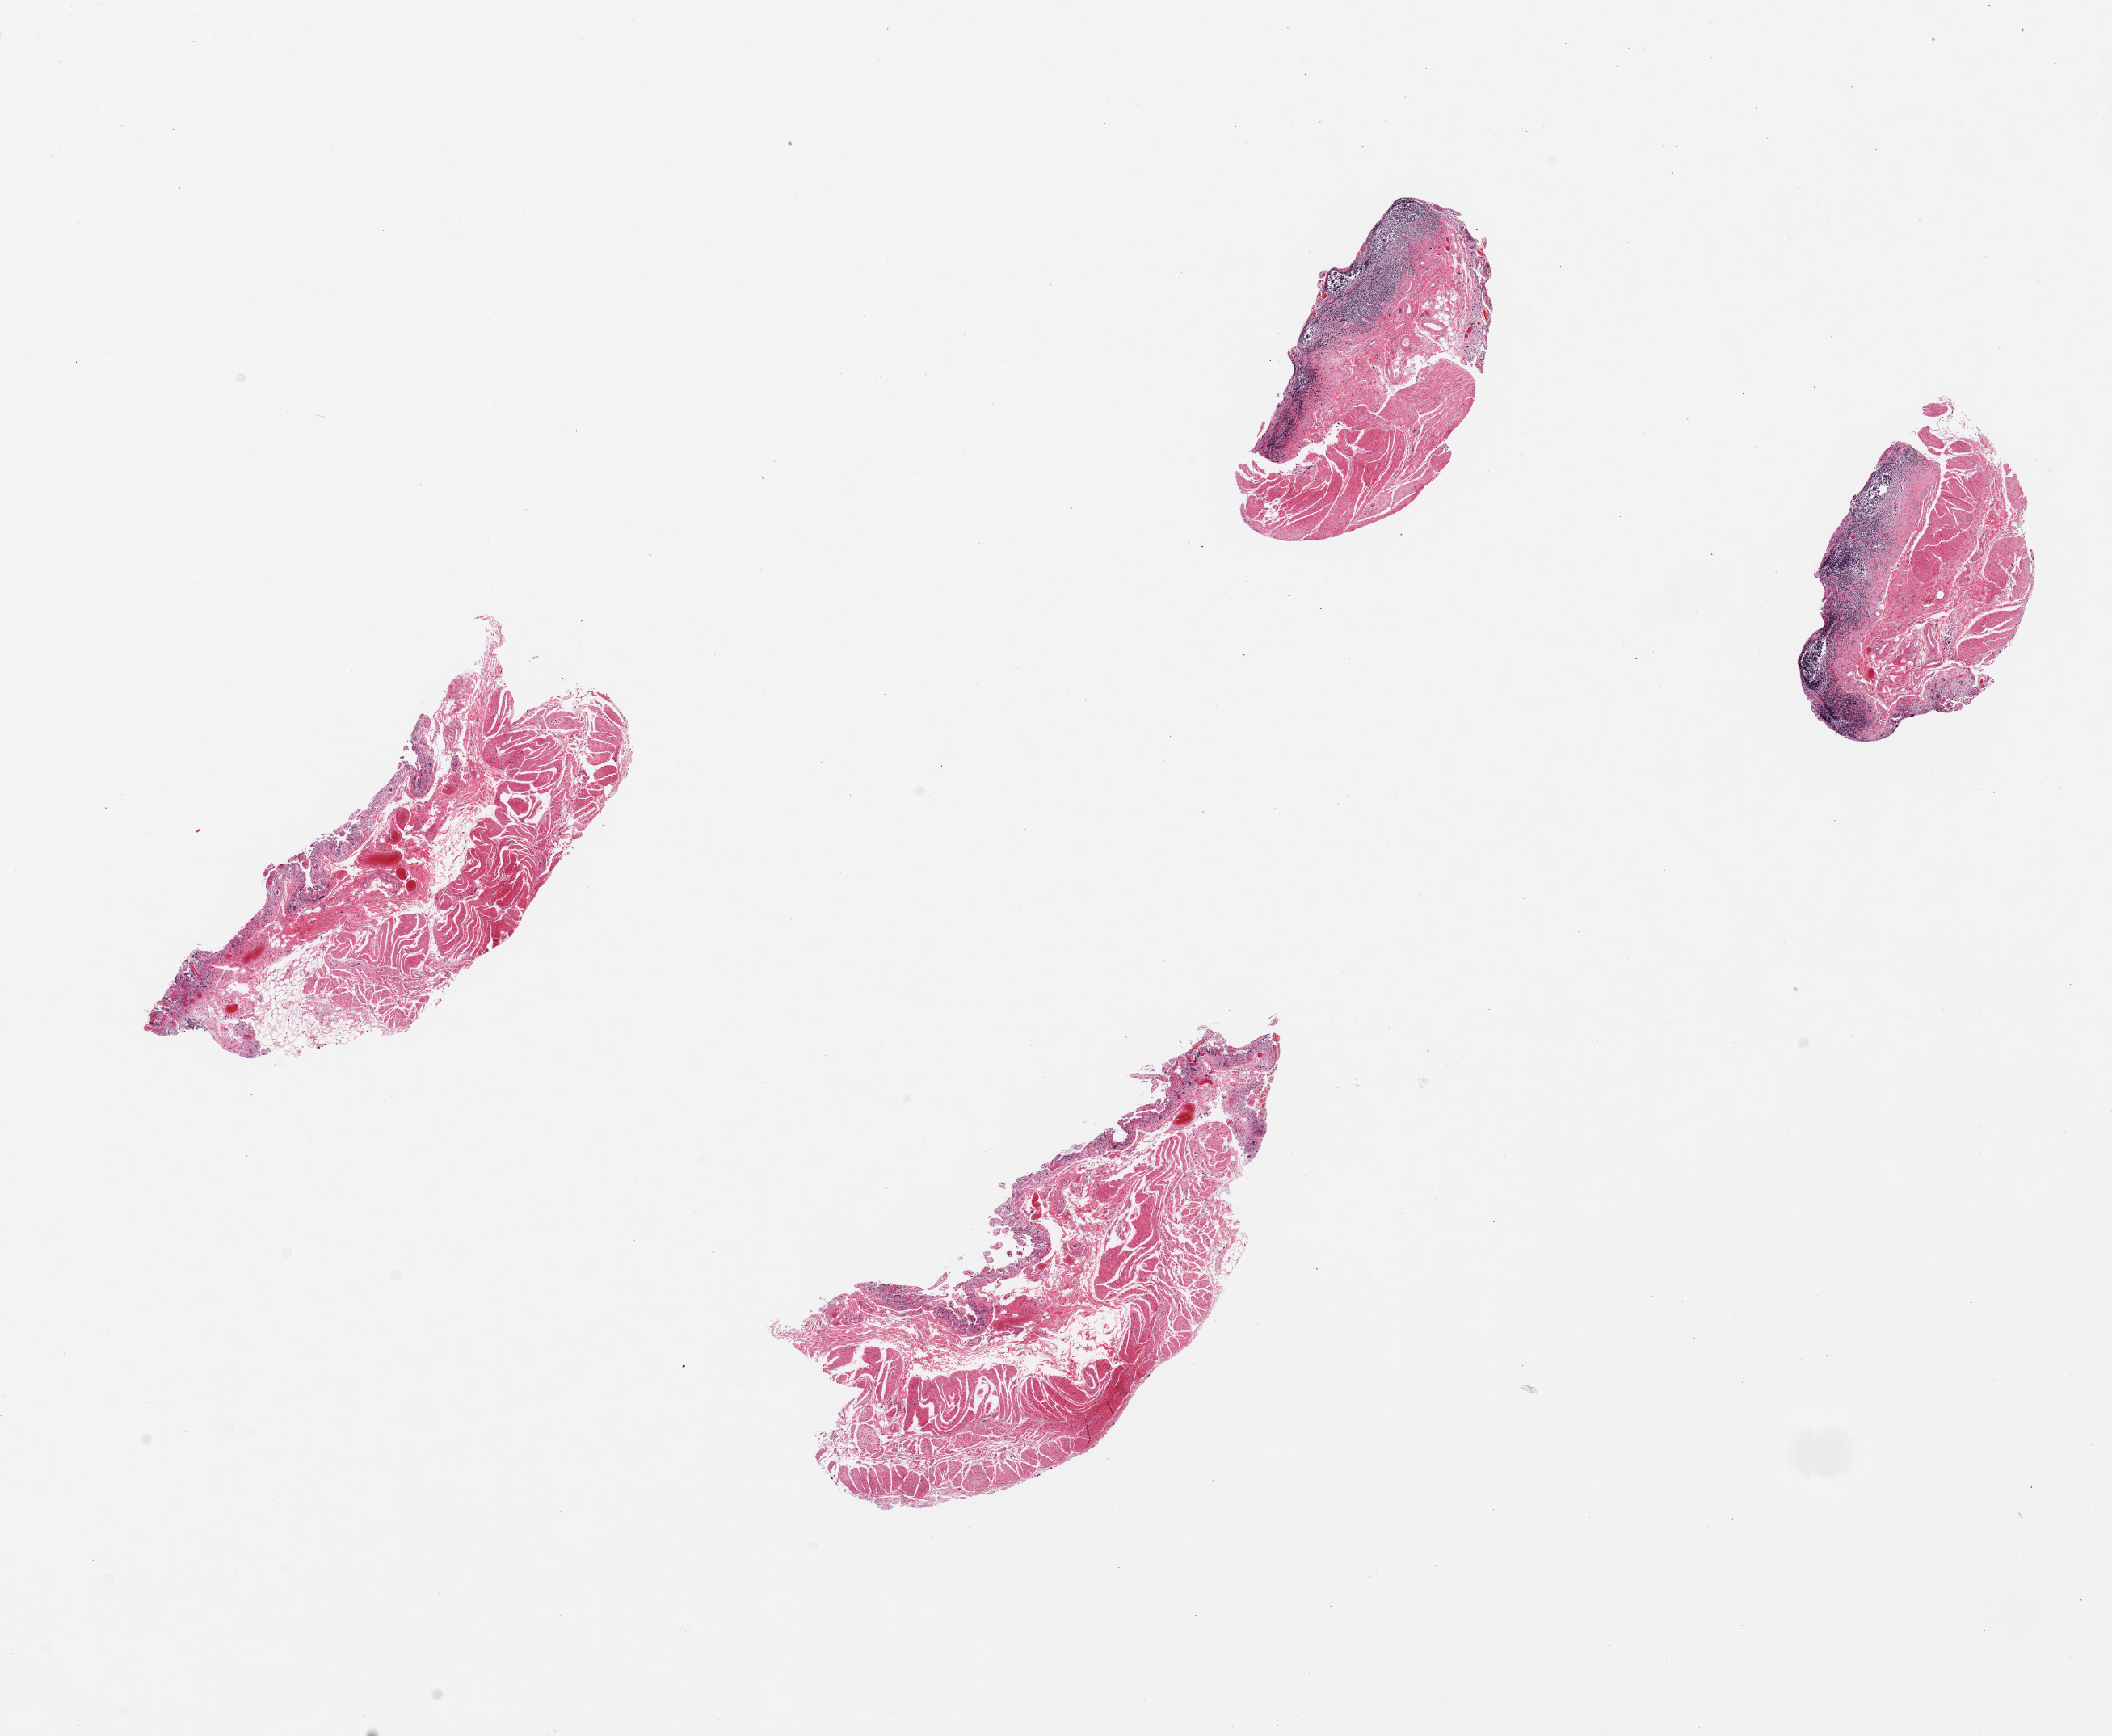
Whole-slide image, haematoxylin and eosin stain, brightfield, shown as a low-resolution overview of the whole scanned area (about 20.7 x 17.0 mm), PAXgene-fixed, paraffin-embedded tissue, target tissue: ileum, tissue donor sample. Donor: male.
Reviewer comment on this tissue sample: 4 pieces, up to 5.5x3mm; mucosa=3;lymphoid=2;muscle=2; 2 have mucosal lymphoid tissue; all have full wall thickness.